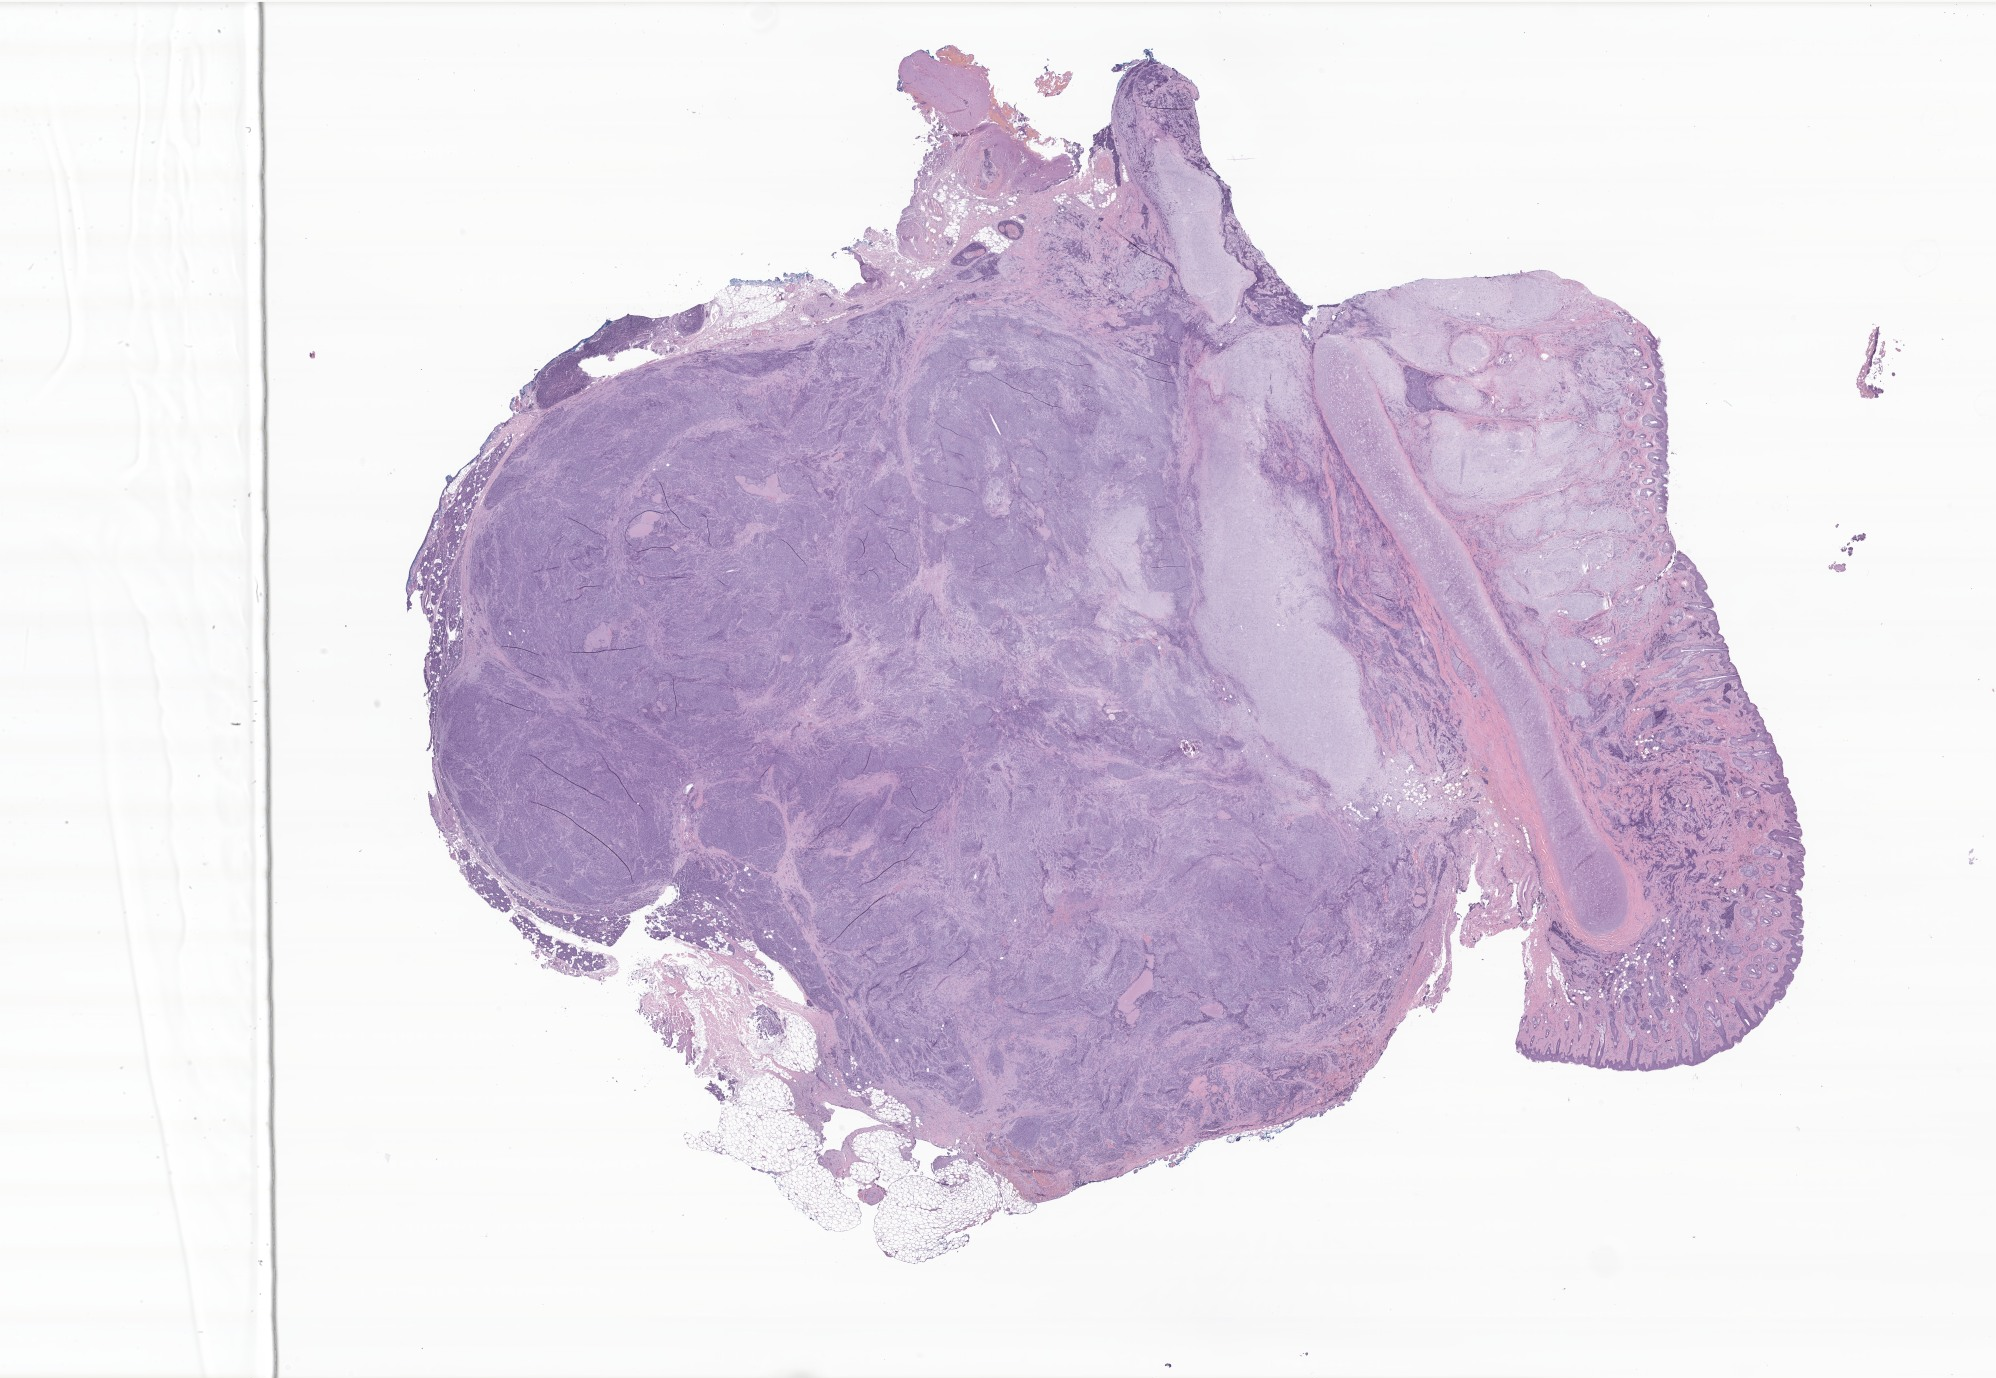
H&E whole-slide image of tumor tissue from the parotid gland, shown as a low-resolution overview of the whole scanned area (about 33.7 x 23.2 mm). Formalin-fixed, paraffin-embedded (FFPE) tissue. Patient: female, age 71 months.
- diagnosis: Carcinoma ex pleomorphic adenoma